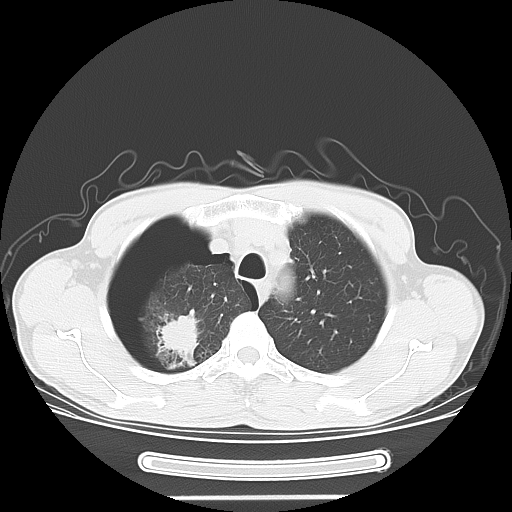
Chest CT, one axial slice; position 54 of 67 along the scan axis; reconstruction kernel LUNG; 120 kVp; lung window (W 1500 / L -600 HU); 5 mm slice thickness; 512 × 512 image matrix, field of view 375 × 375 mm. Male patient. Case-level facts recorded for this patient, not image findings: clinical TNM (as recorded): T1c N0 M0.
Outlined on this slice (rectangle marked by the reading radiologist):
- lung tumour (recorded histology: adenocarcinoma): bounding box <154,303,199,365> (left, top, right, bottom; pixels)